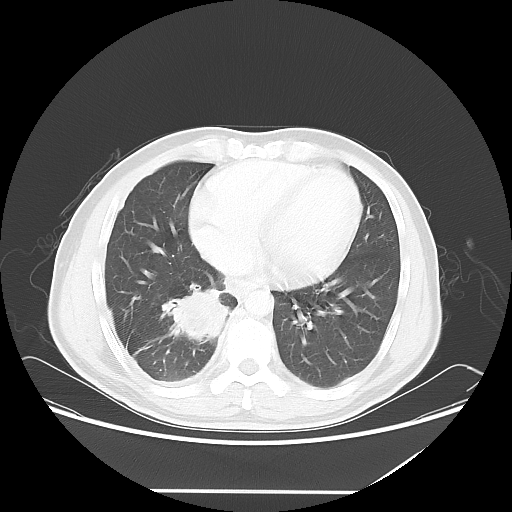
Chest CT, one axial slice; lung window (W 1500 / L -600 HU); 5 mm slice thickness; 512 × 512 image matrix. Male patient, age 48 years. Case-level facts recorded for this patient, not image findings: clinical TNM (as recorded): T3 N3 M1a.
Outlined on this slice (bounding box drawn by a radiologist):
- lung tumour (recorded histology: squamous cell carcinoma): box from (x=152, y=282) to (x=232, y=347) px